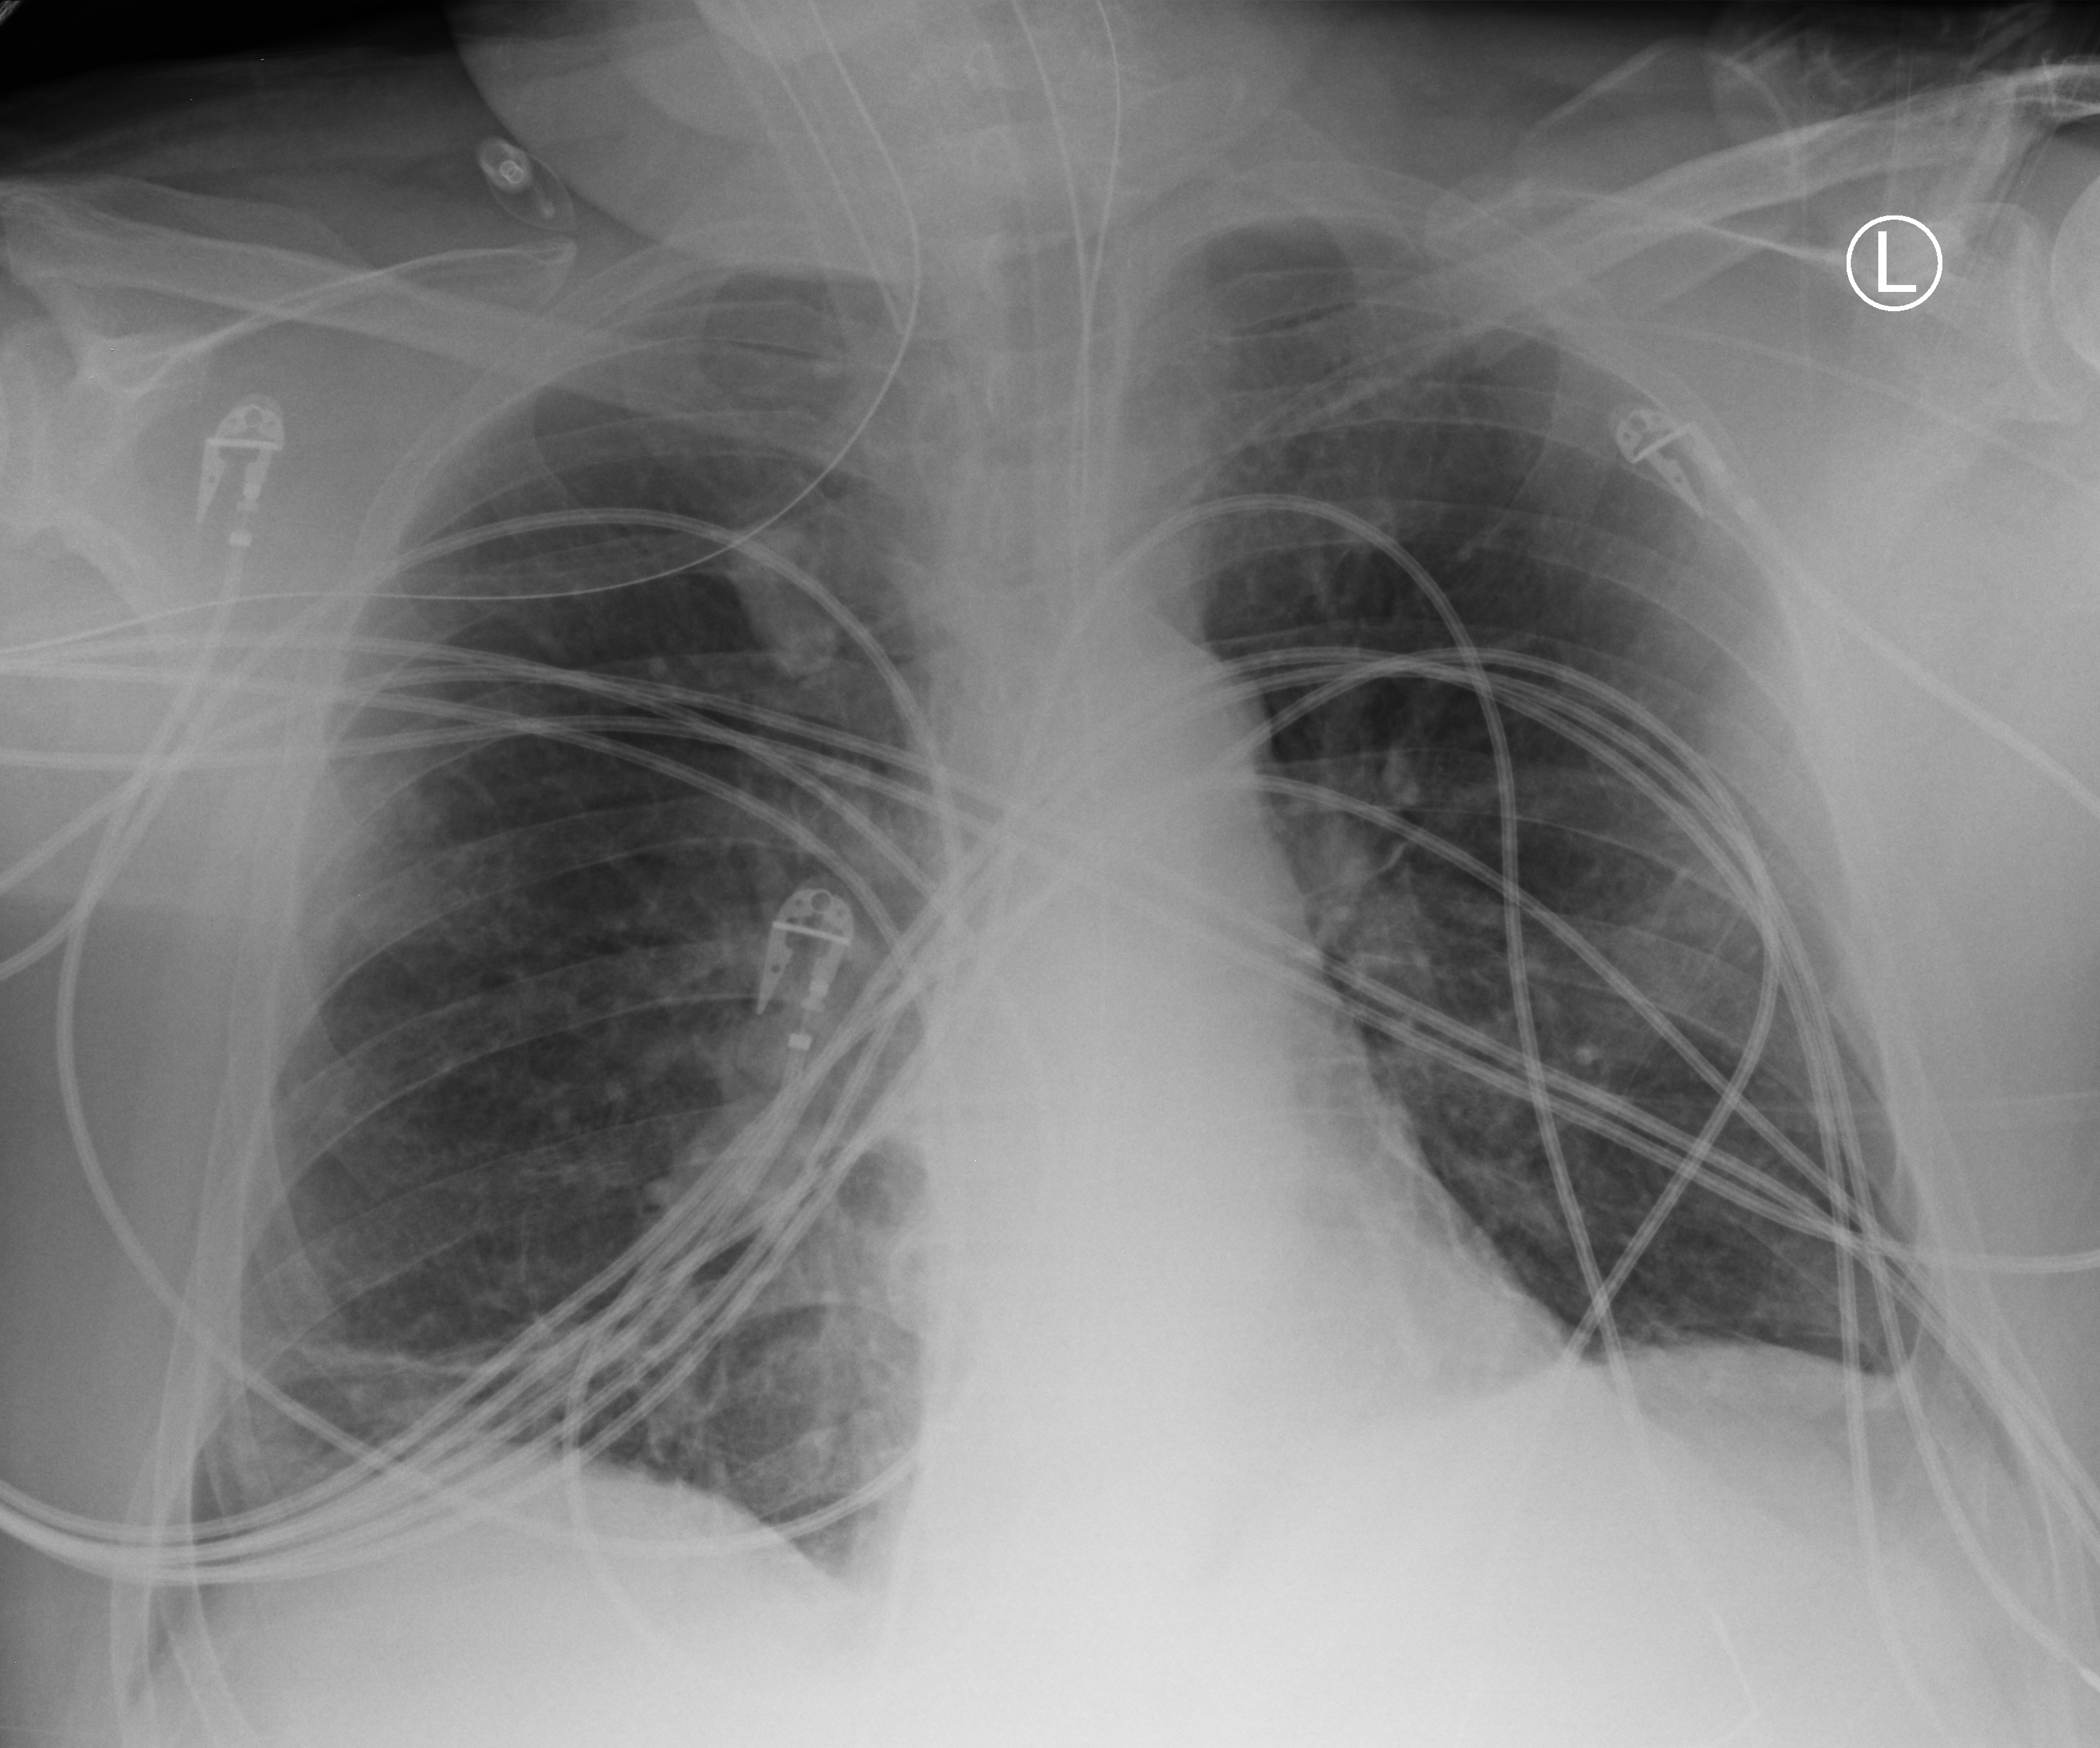
Chest X-ray (portable), anteroposterior (AP) projection. Male patient hospitalised with COVID-19, age 60–74 years.
Hospital-stay facts (about this admission, not read from this image; timing relative to this image not recorded):
- length of hospital stay: 22 days
- admitted to intensive care during this hospital stay: yes
- mechanically ventilated during this hospital stay: yes